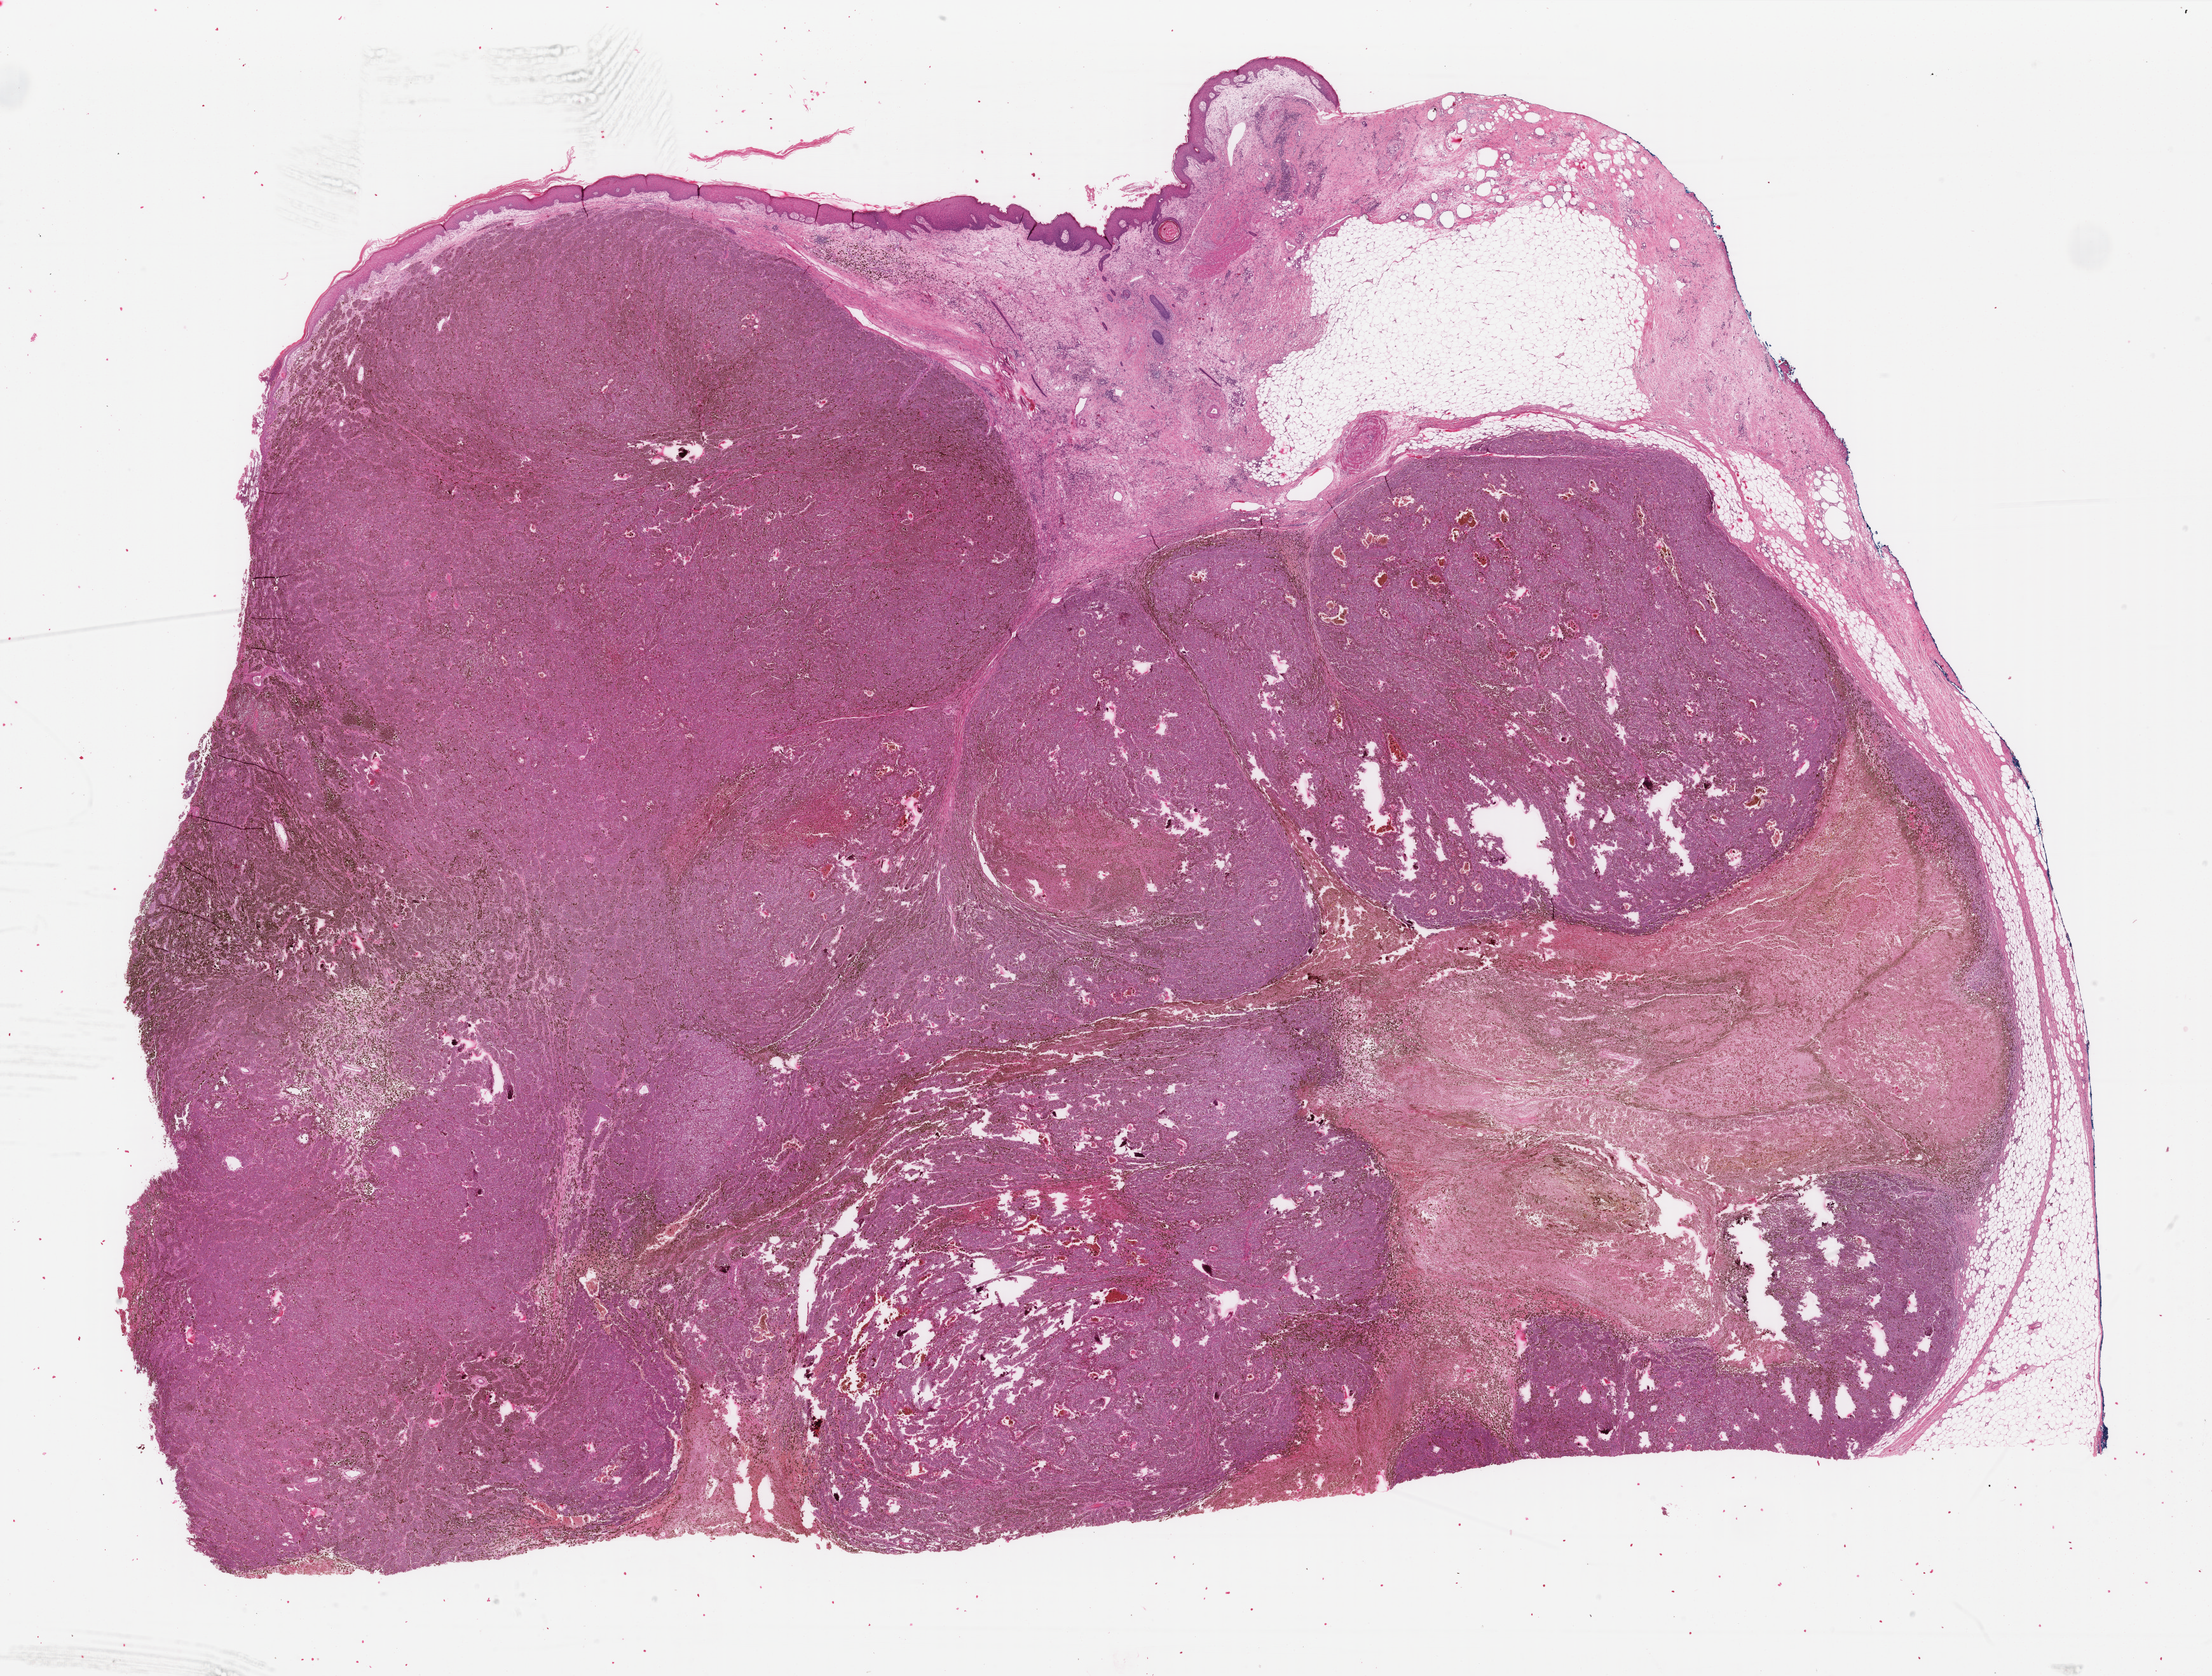
H&E-stained whole-slide image — low-resolution overview of the scanned area, about 27.6 x 20.9 mm (from a 40x scan). FFPE section. Sample: primary tumour, skin. Female, age 84 years at initial diagnosis.
- diagnosis: Malignant melanoma, NOS